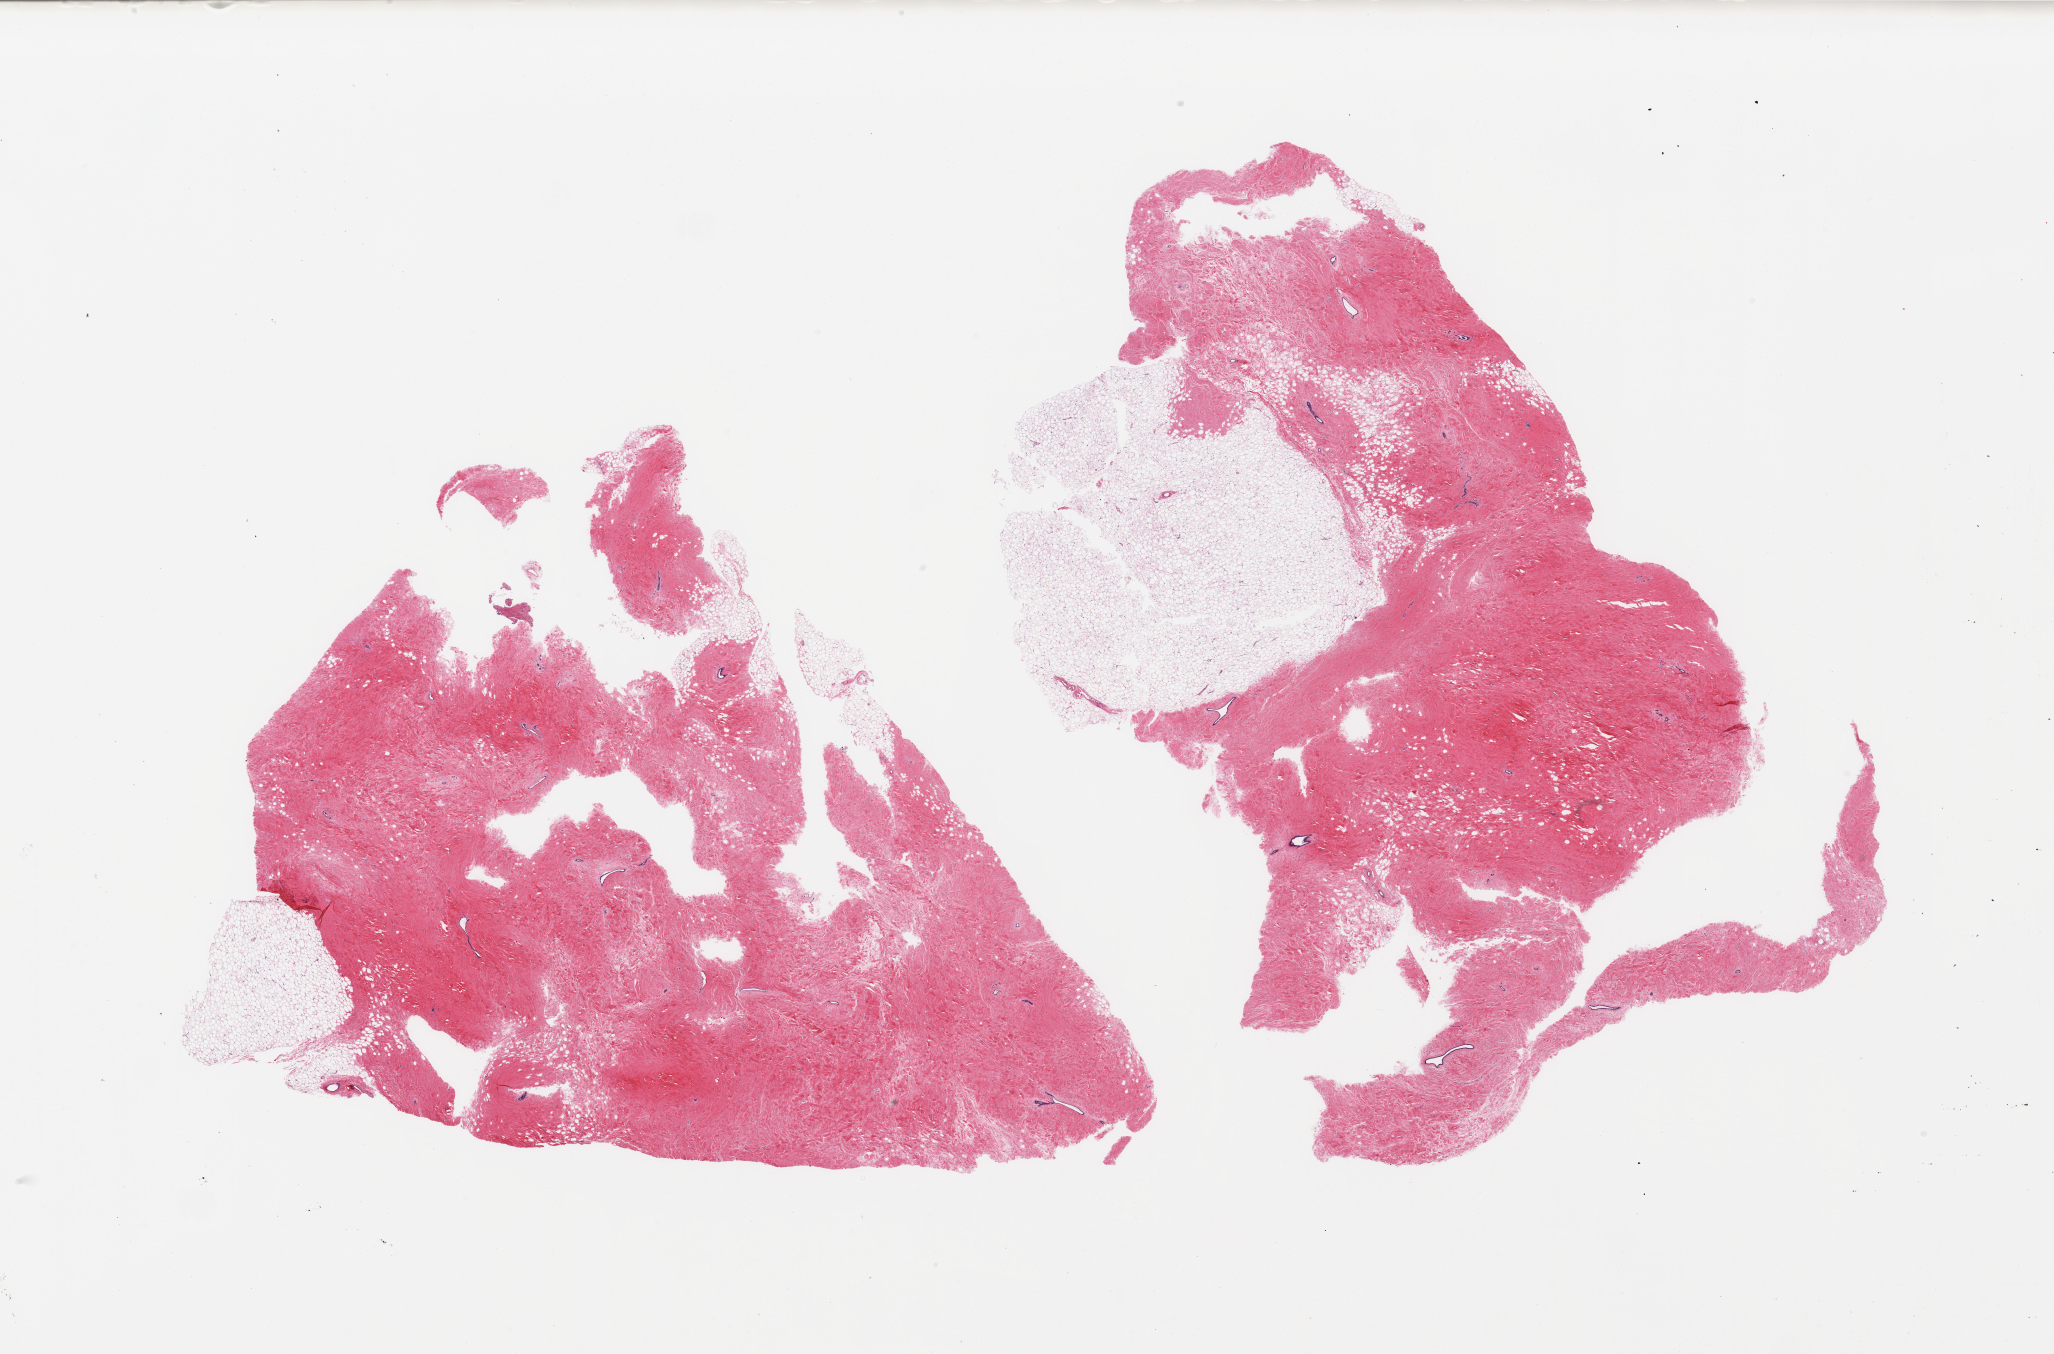
Whole-slide image, hematoxylin and eosin (H&E) stain — low-resolution overview of the scanned area, about 32.5 x 21.4 mm, PAXgene-fixed paraffin-embedded (PFPE) section, target tissue: breast, tissue donor sample. Female donor.
Reviewer comment on this tissue sample: 2 pieces; 90% and 60% dense fibrous stroma with rare ductal structures and 10% and 40% adipose tissue.